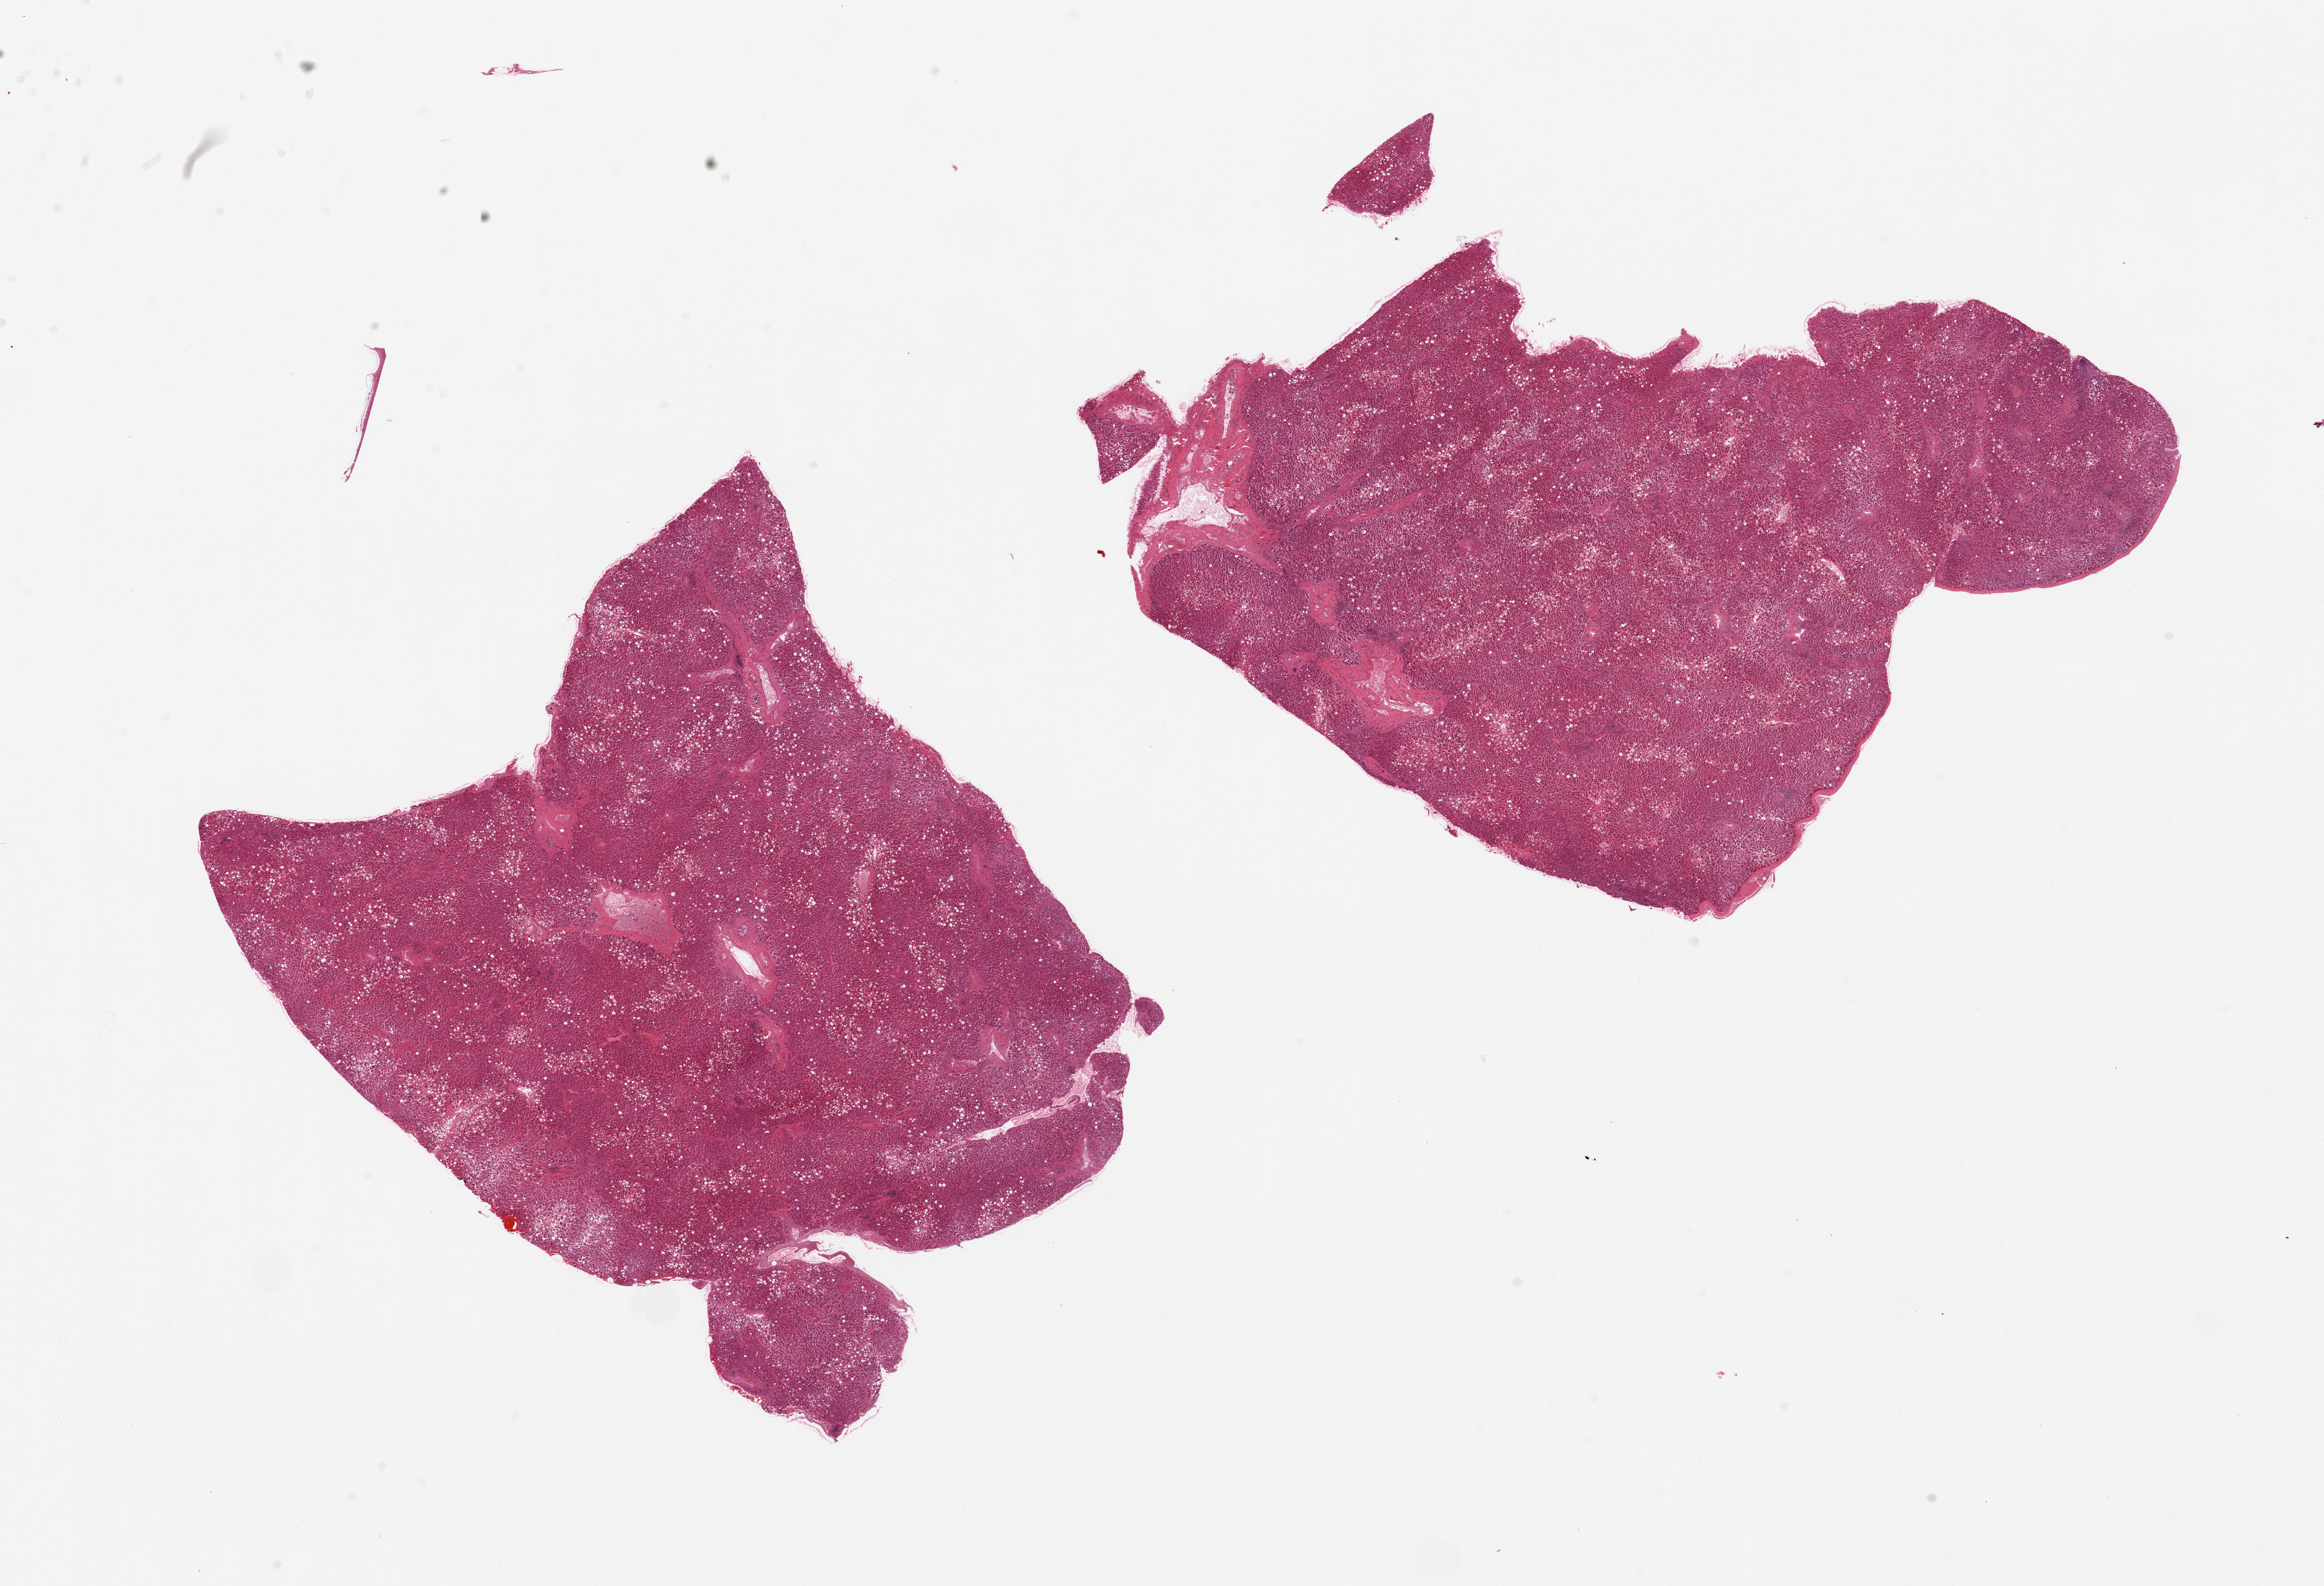
Haematoxylin and eosin whole-slide image — a low-resolution overview of the entire scanned area, about 28.5 x 19.5 mm; PAXgene-fixed paraffin-embedded (PFPE) section; section of liver (target tissue); tissue donor sample.
Reviewer comment on this tissue sample: 2 pieces, predominantly macrovesicular steatosis, includes capsule (target is 1 cm below capsule).